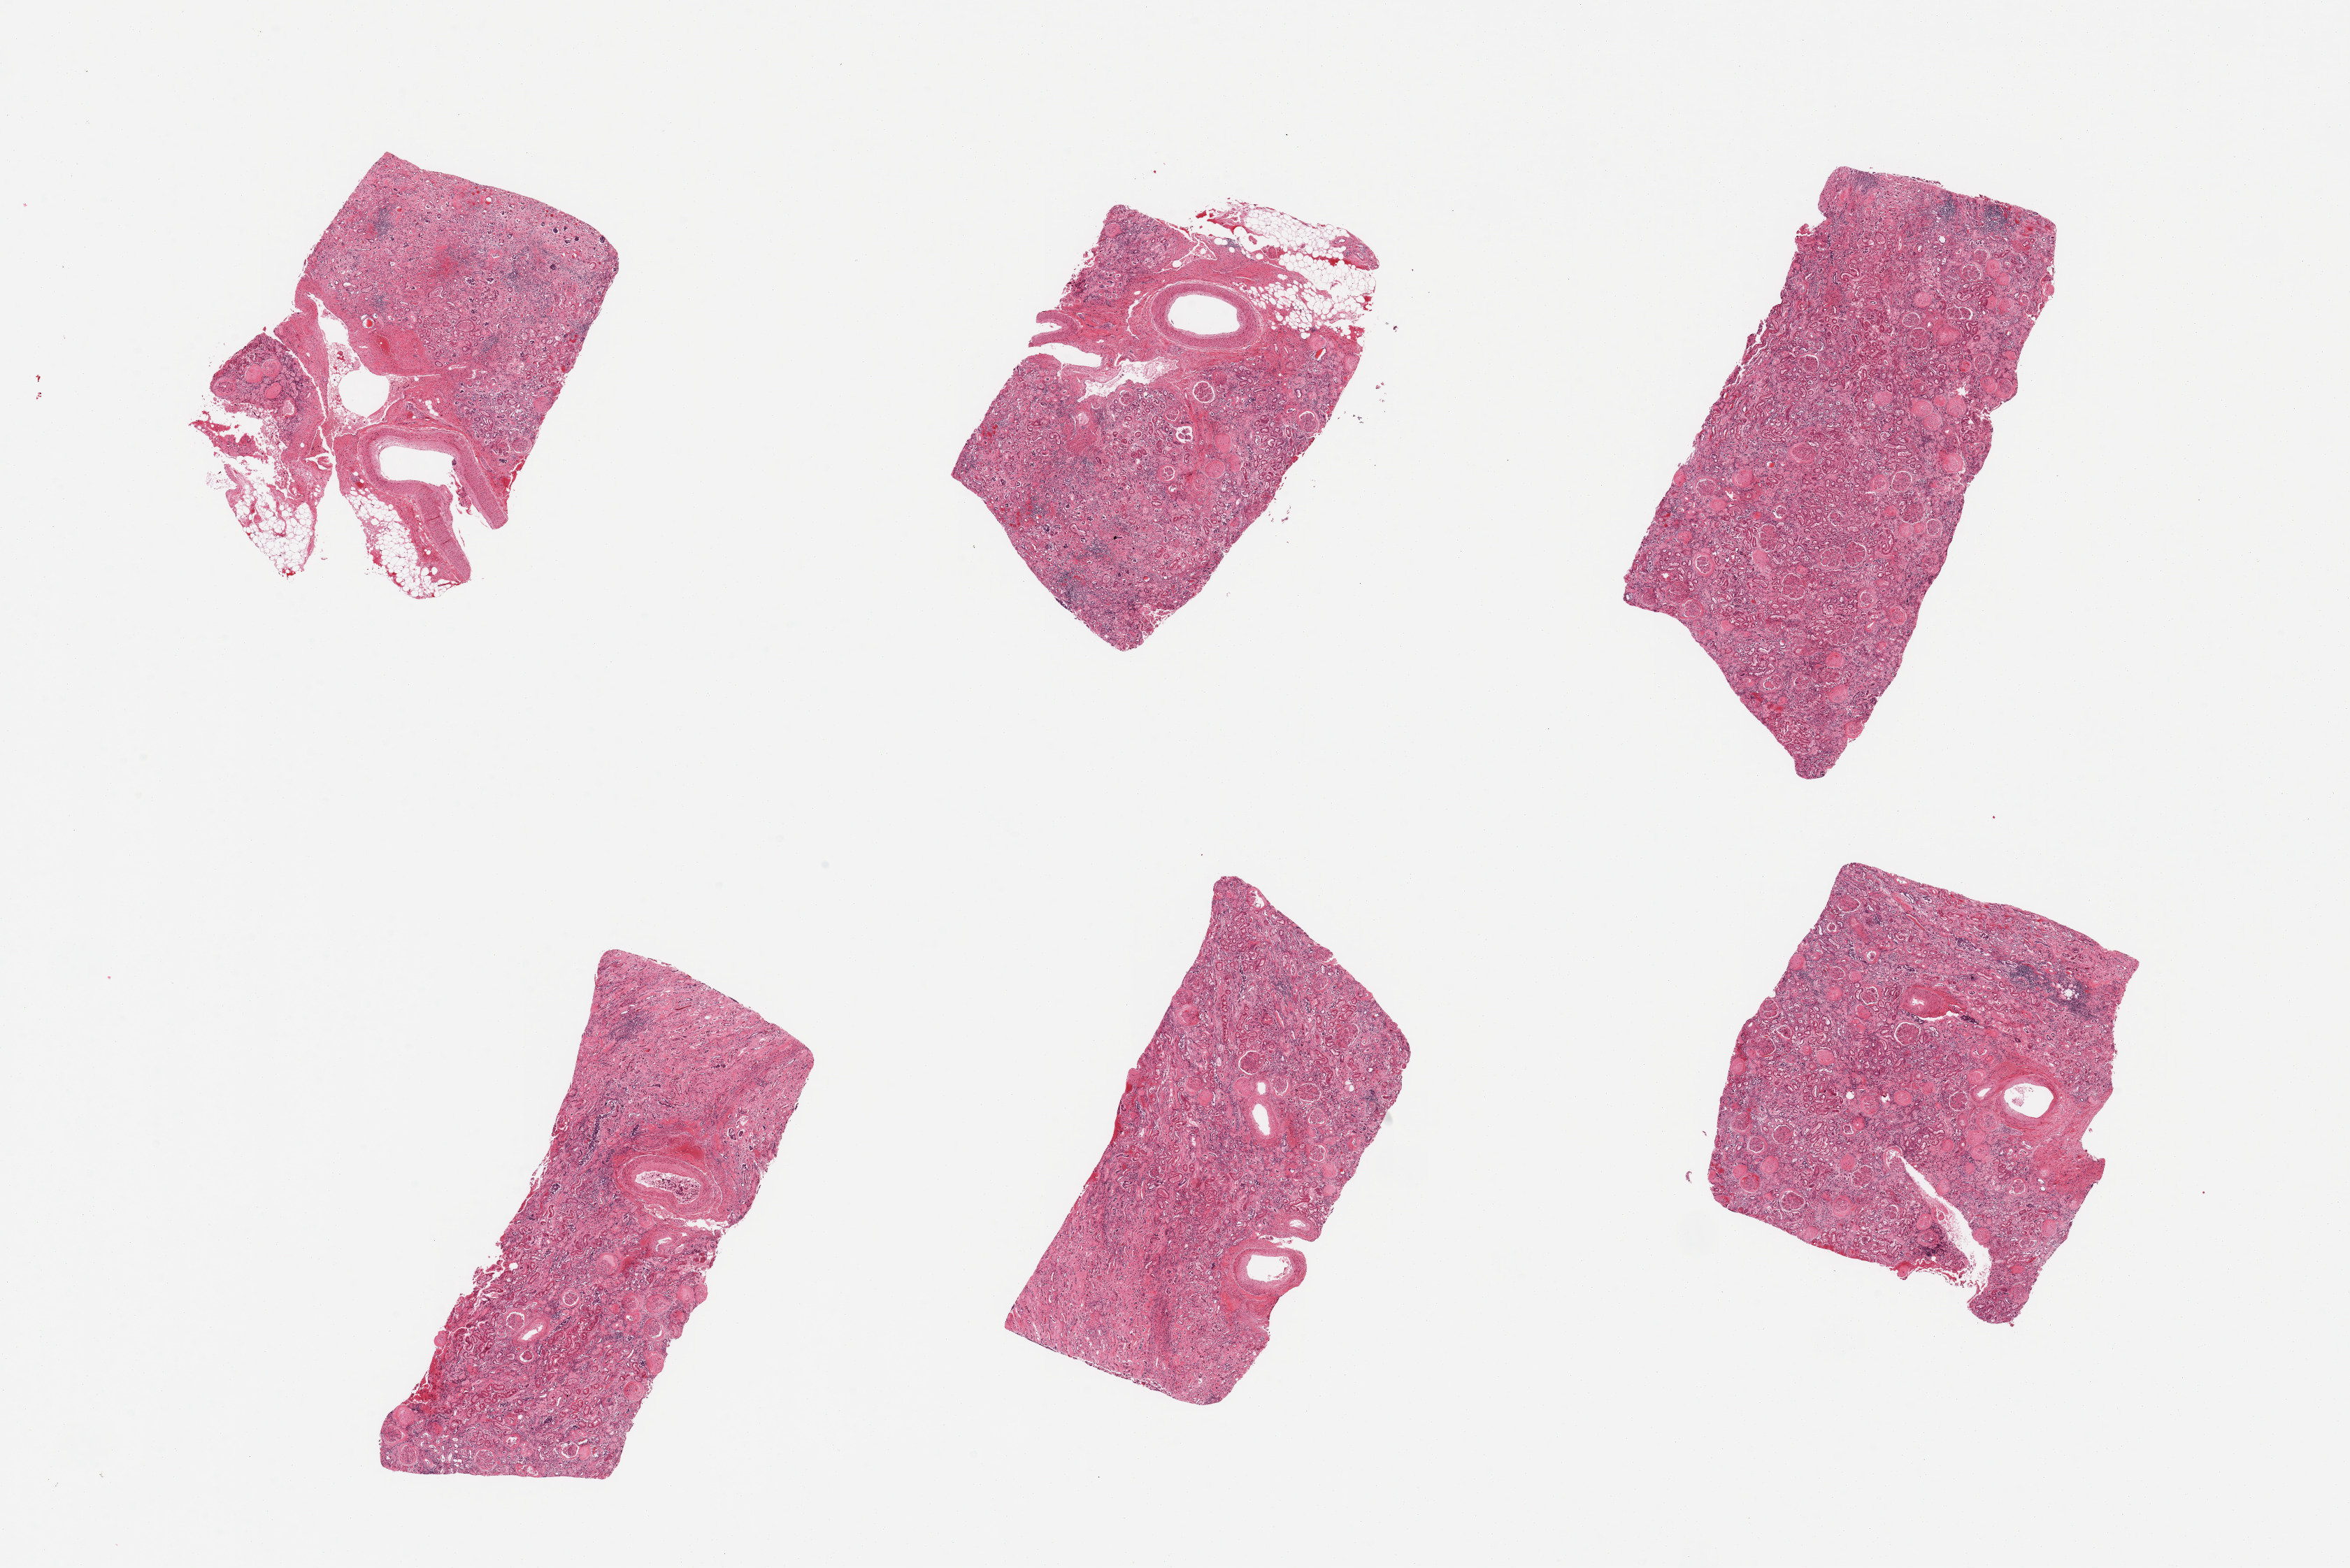
Hematoxylin and eosin (H&E) whole-slide image, brightfield — a low-resolution overview of the entire scanned area, about 26.6 x 17.7 mm (slide scanned at 20x). PAXgene-fixed paraffin-embedded (PFPE) section. Target tissue: renal cortex. Tissue donor sample. Donor sex: female.
Reviewer comment on this tissue sample: 6 pieces; advanced nodular glomerulosclerosis consistent with diabetes; limited value due to disease.